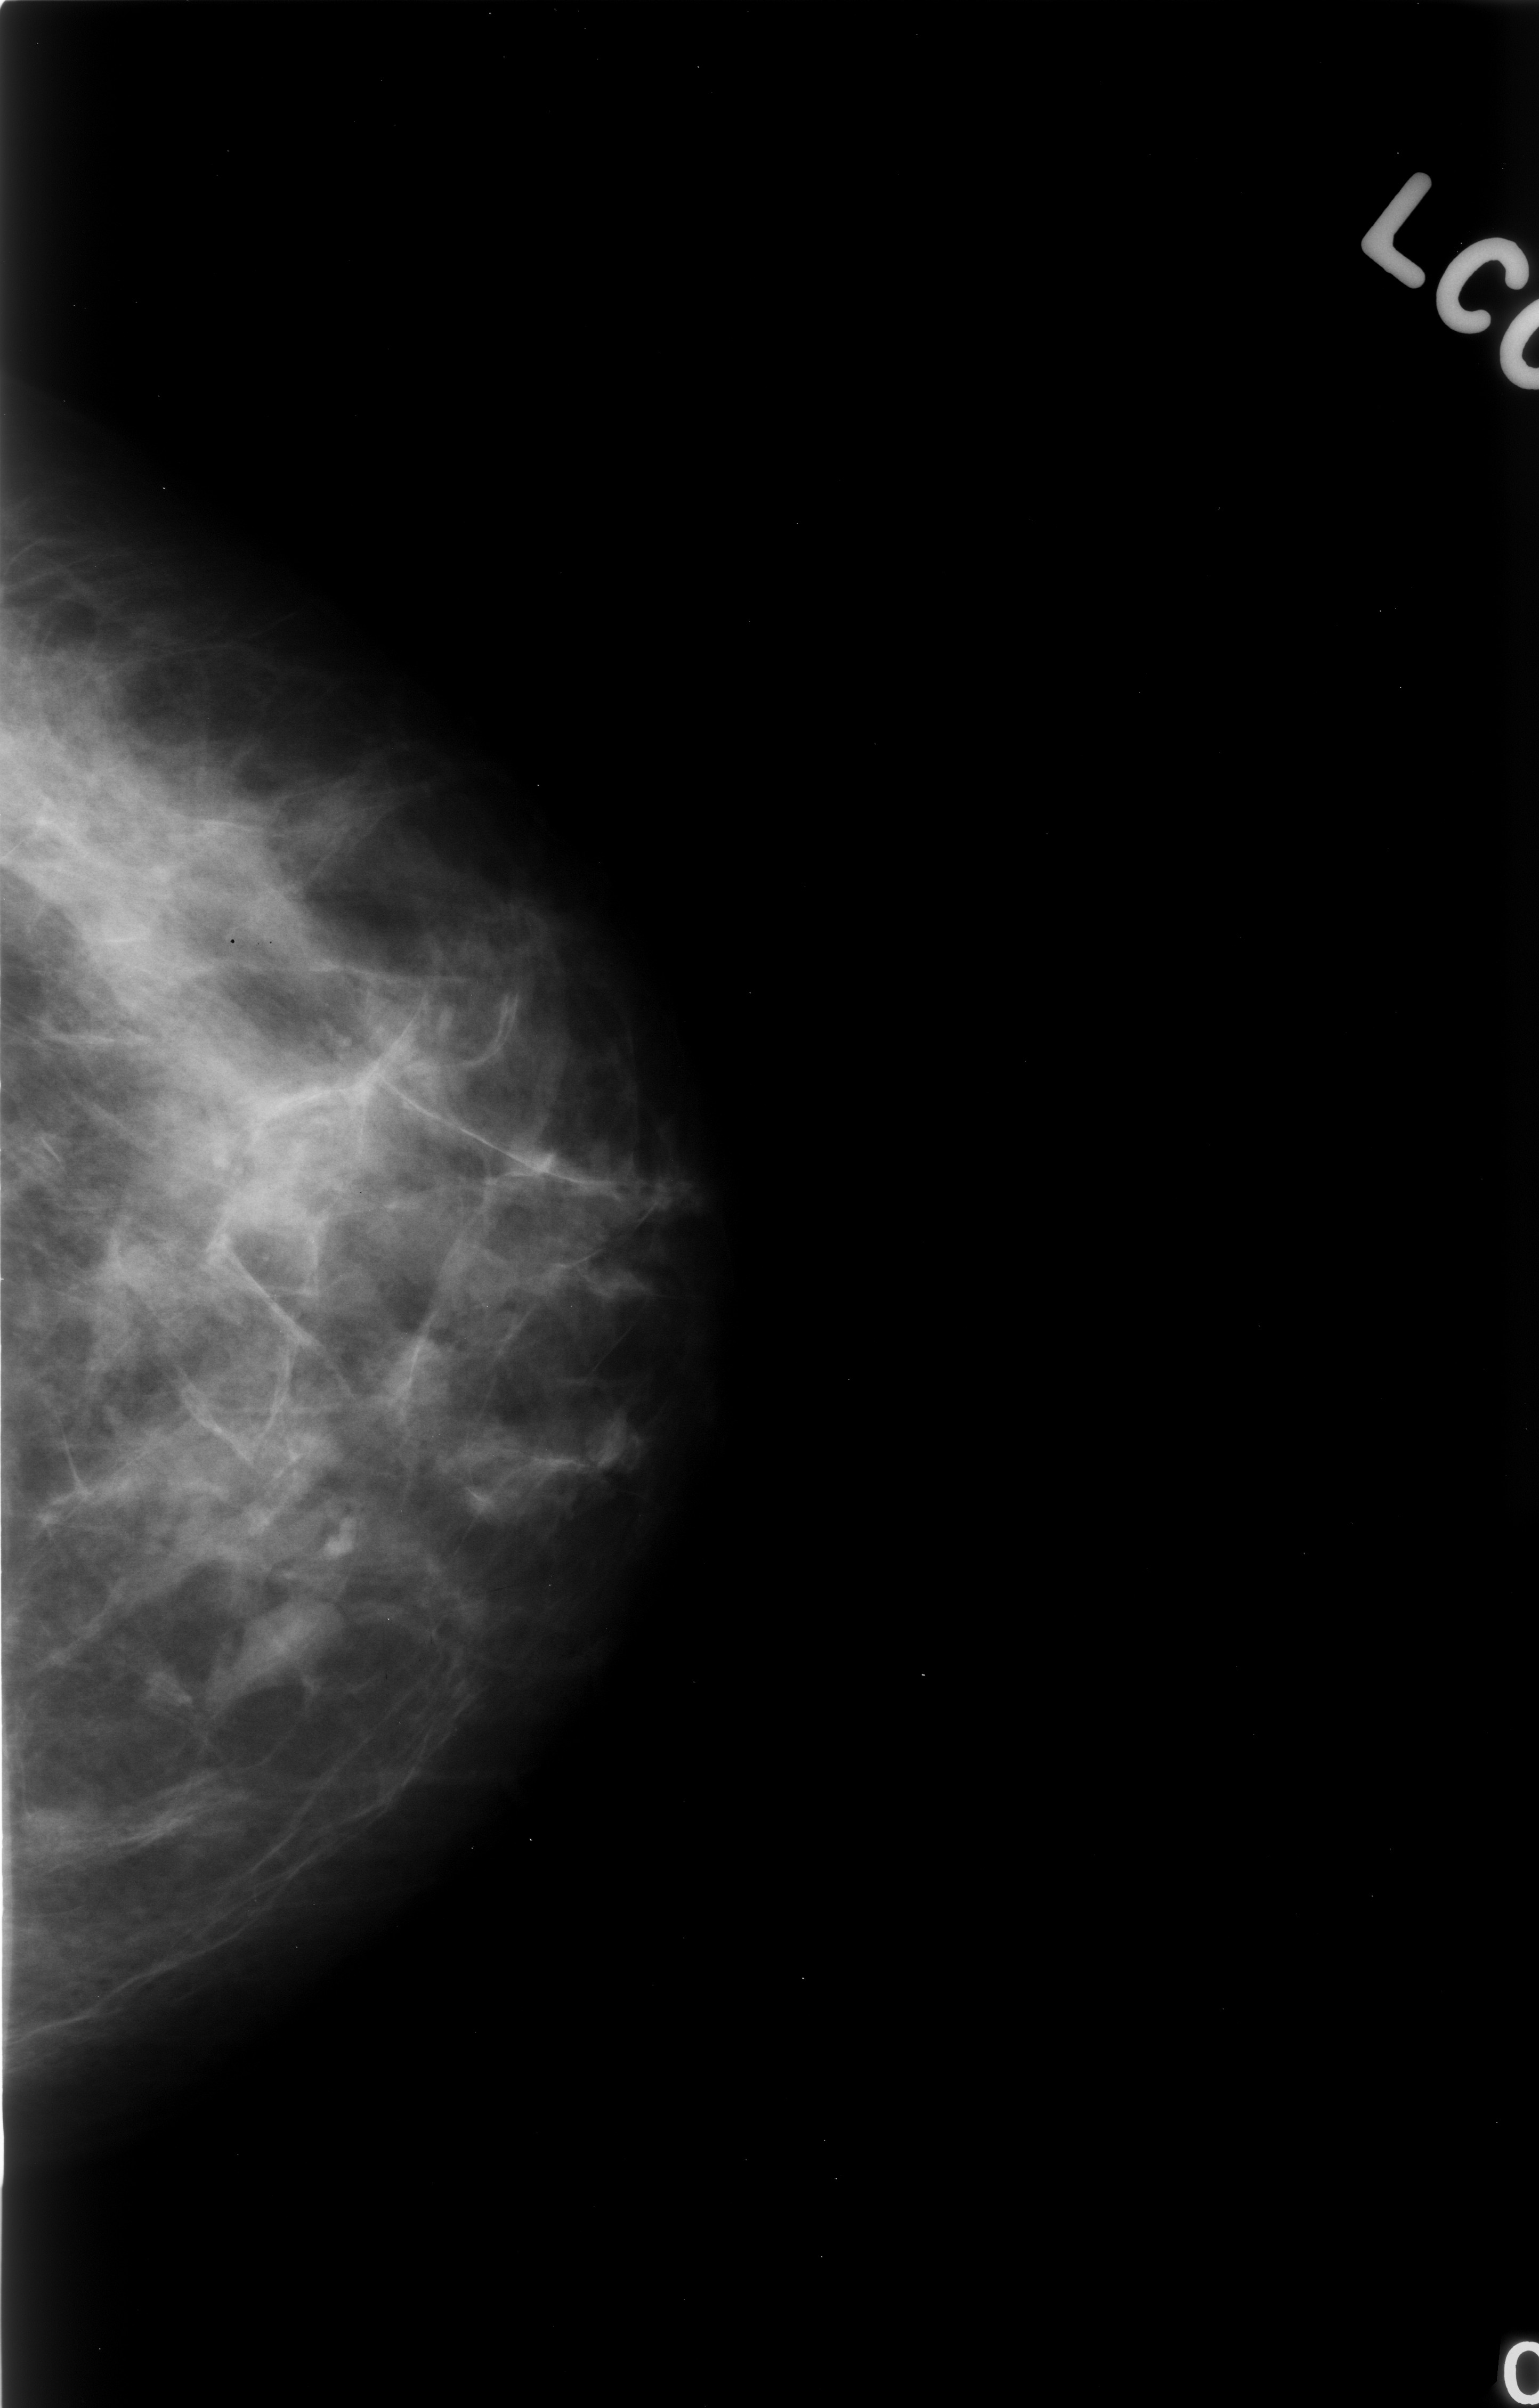
Scanned film-screen mammogram; left breast; craniocaudal (CC) view; breast composition: scattered fibroglandular densities (BI-RADS density category 2 of 4); 1539 × 2408 image matrix.
Expert-marked regions of interest on this image (one box per marked abnormality):
- mass, shape lobulated, margins circumscribed; BI-RADS assessment category 3; subtlety rating 5 on a 1 (subtle) to 5 (obvious) scale; pathology (as recorded): benign: bounding box [x1, y1, x2, y2] px = [233, 1604, 329, 1689]